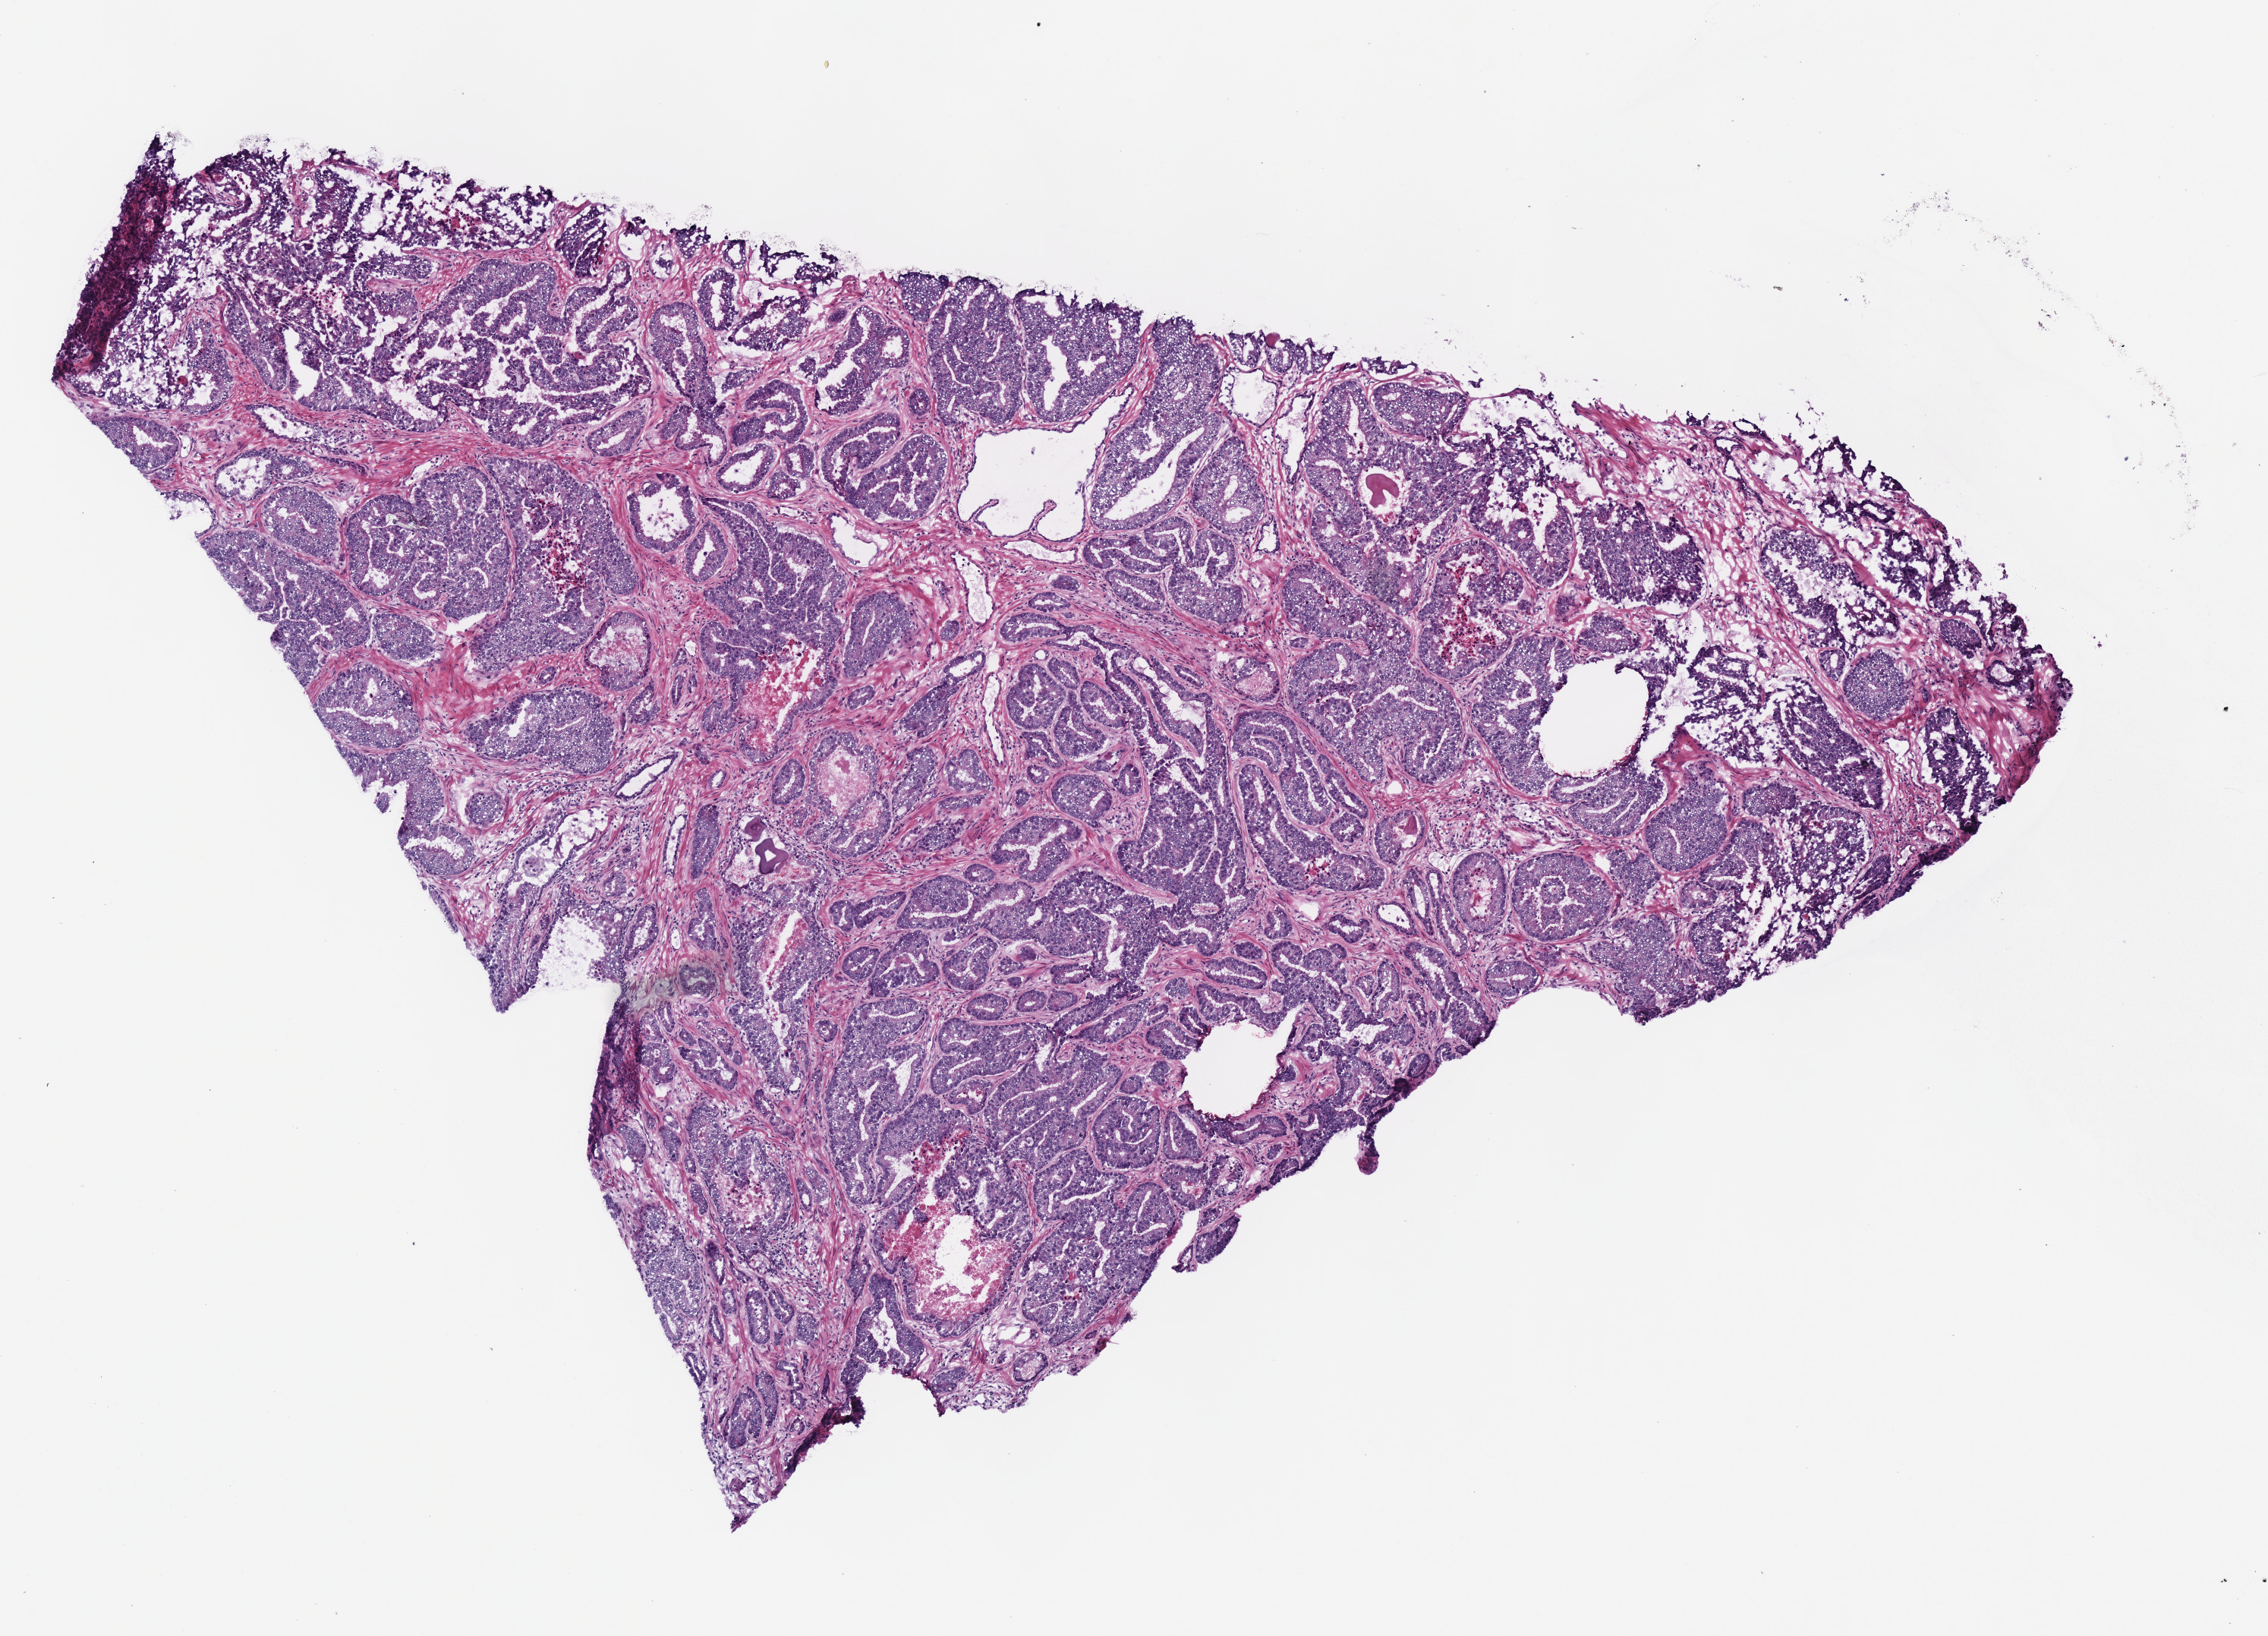
H&E-stained whole-slide image, shown as a low-resolution overview of the whole scanned area (about 5.9 x 4.2 mm, from a 40x scan); frozen section; primary tumour sample from the prostate. Male, age 46 years at initial diagnosis. Gleason score: 7 (4+3).
- diagnosis: Acinar cell carcinoma (prostate gland)